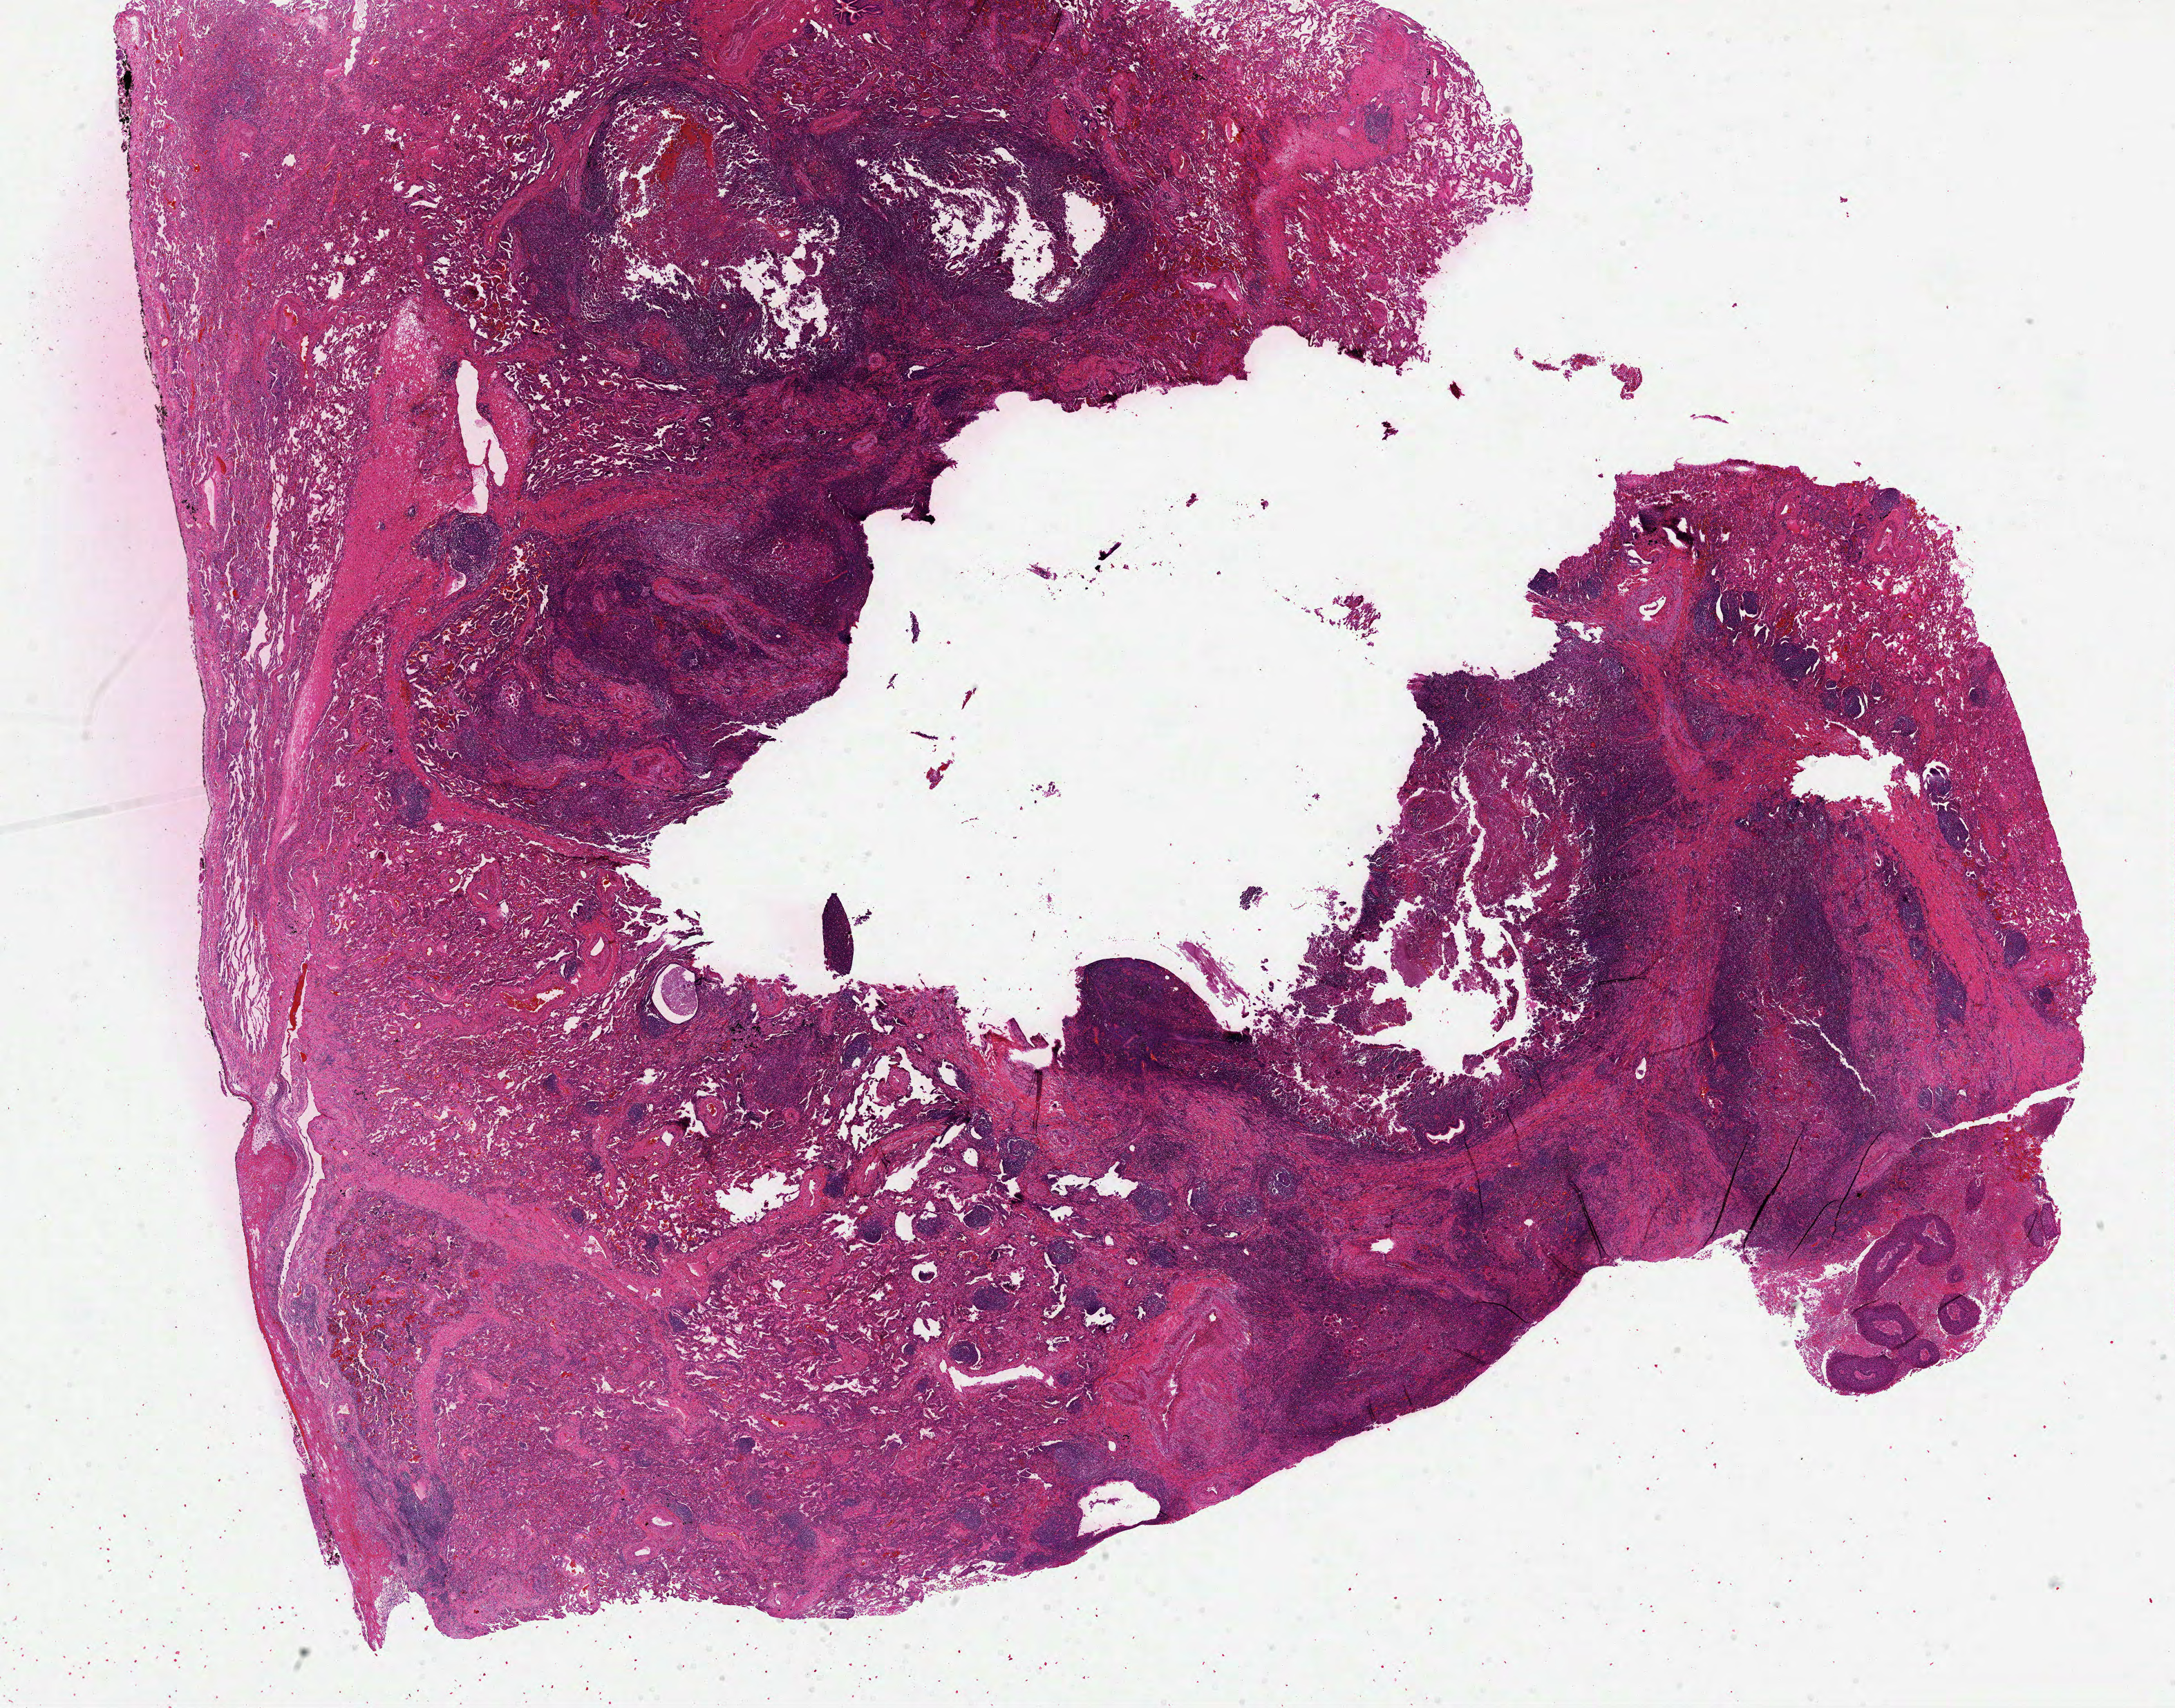
Whole-slide histology image, H&E — whole scanned area (about 25.4 x 19.9 mm, acquisition: 40x scan) shown as a low-resolution overview. Formalin-fixed paraffin-embedded (FFPE) diagnostic section. Primary tumour sample from the lung. Patient: male, age at initial diagnosis 73 years.
Laterality: left. Pathologic diagnosis: Squamous cell carcinoma, NOS (lower lobe, lung). AJCC pathologic stage: IA (5th edition).